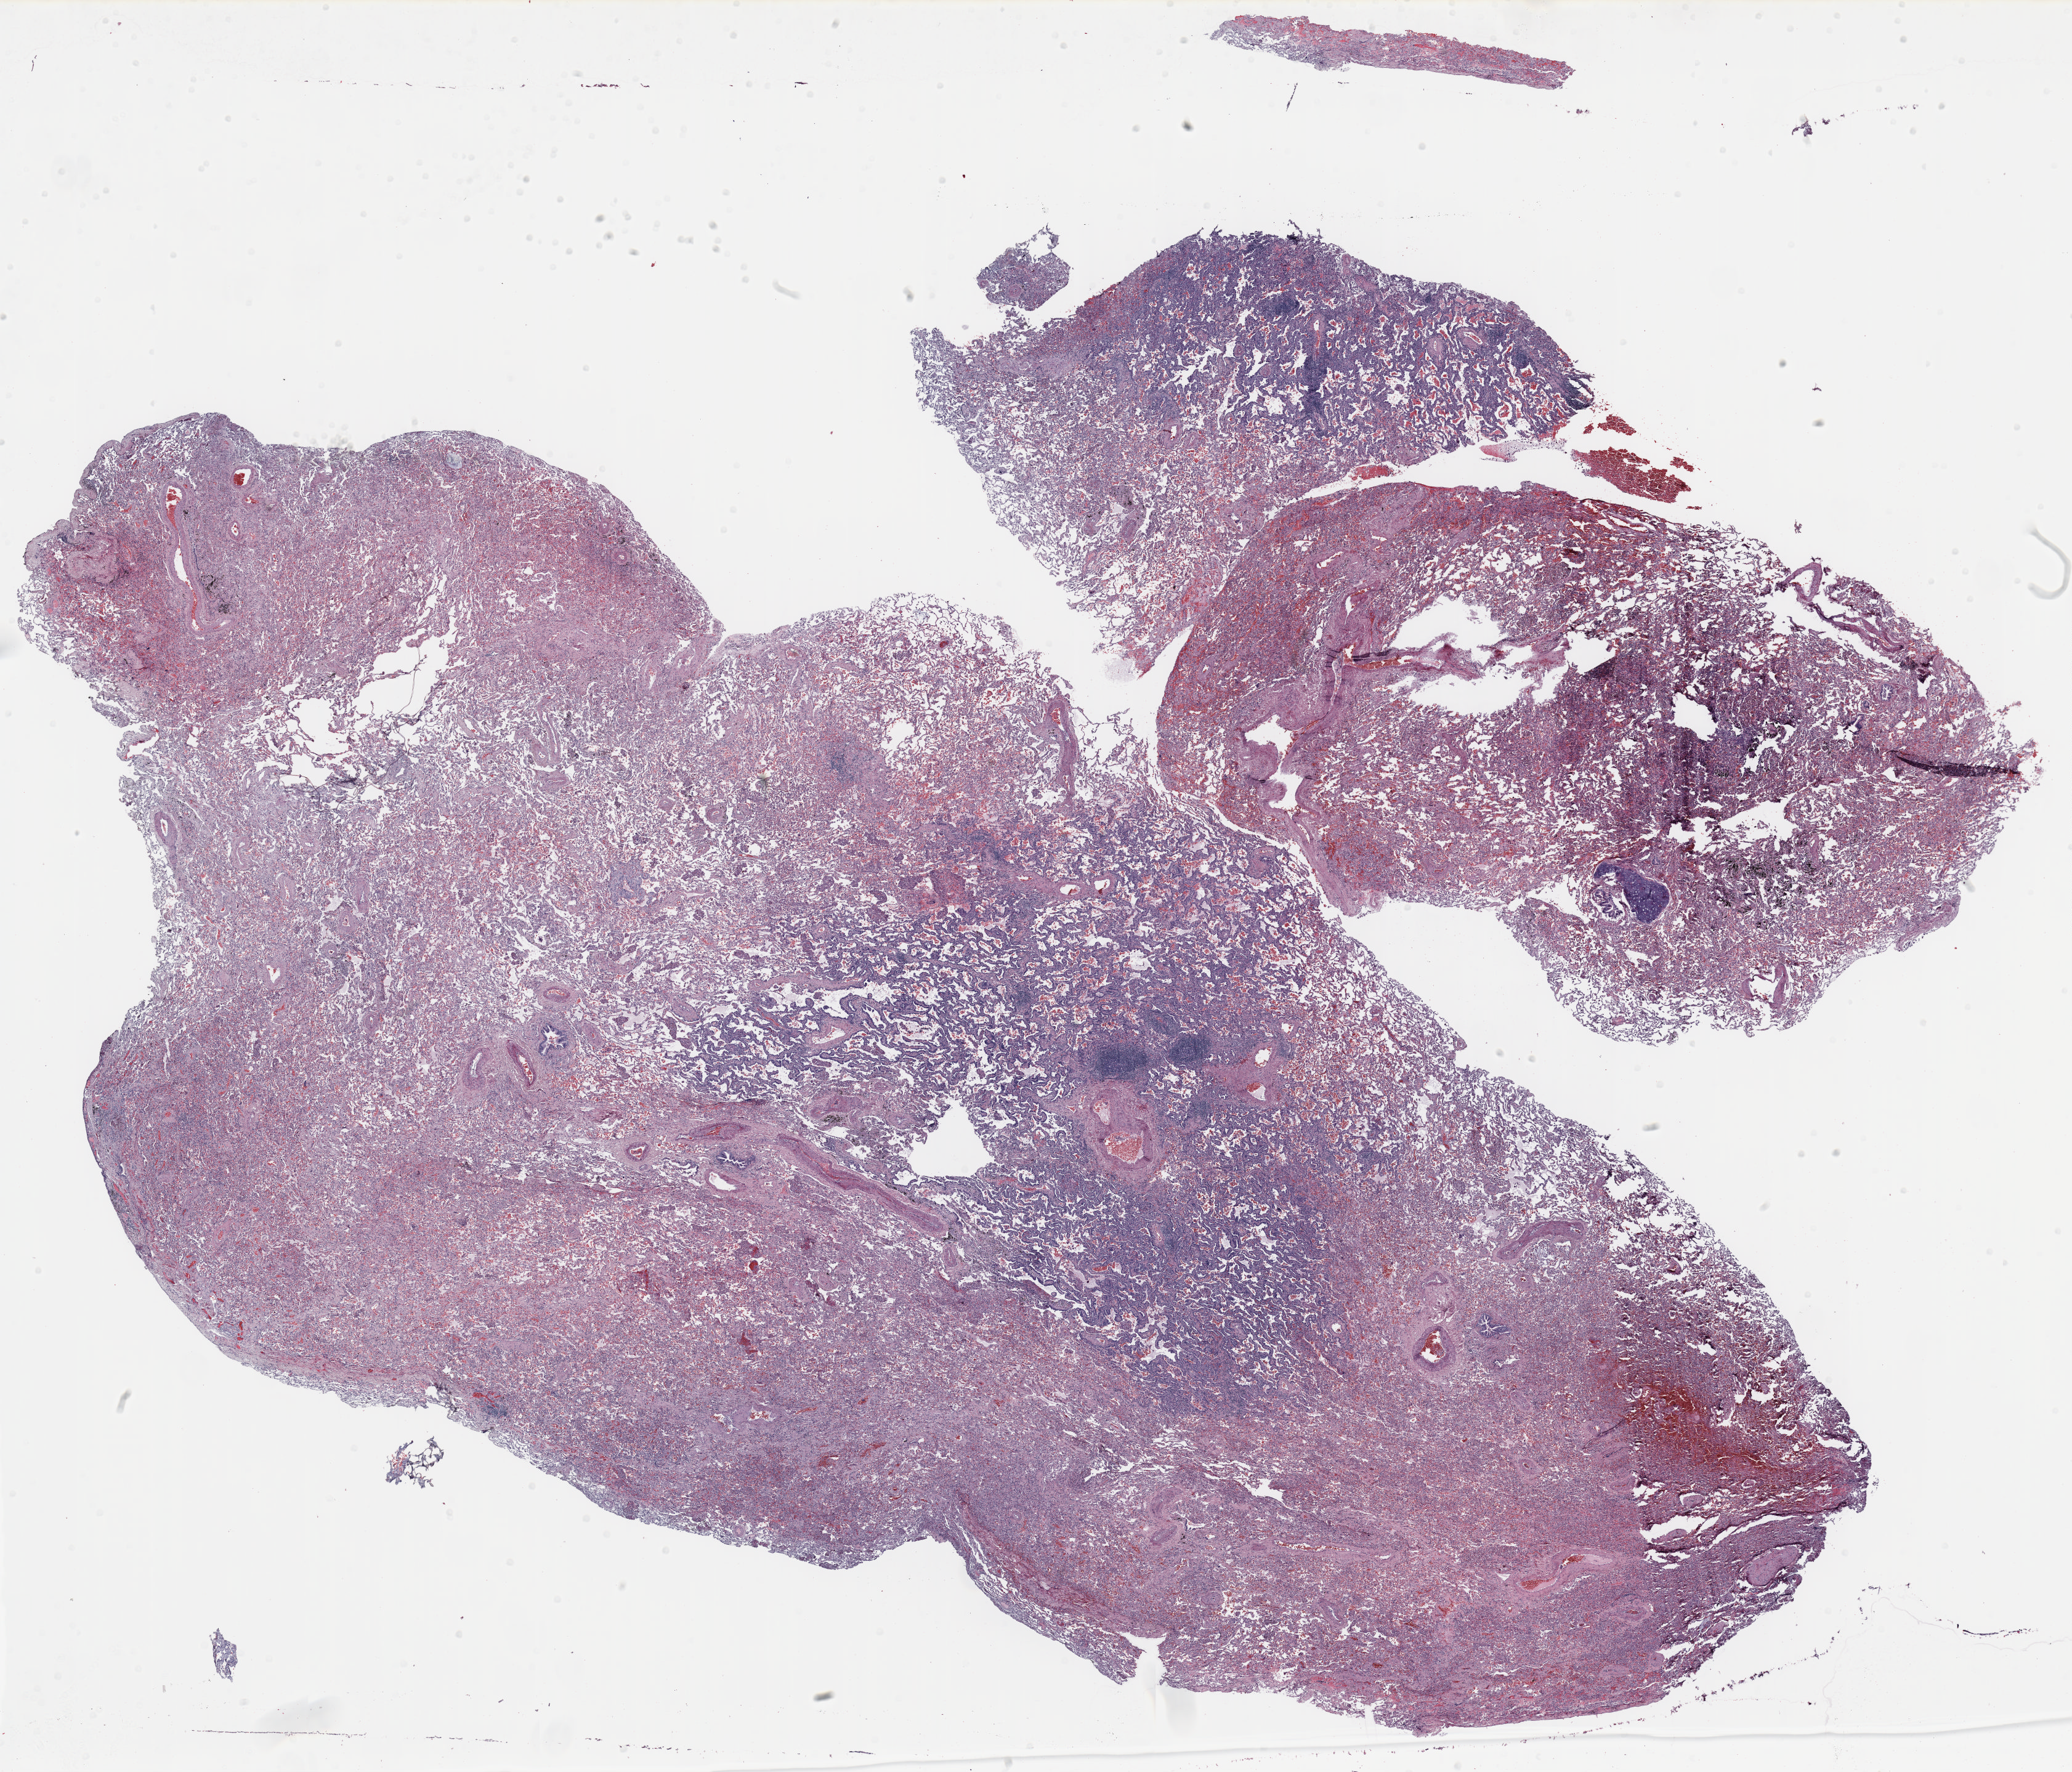
Whole-slide histology image, Hematoxylin and eosin (H&E) stained, whole scanned area (about 27.0 x 23.1 mm, from a 20x scan) shown as a low-resolution overview, formalin-fixed paraffin-embedded (FFPE) section, lung tissue. Male, age 59 at enrolment. Current smoker at enrolment.
Primary tumour location (clinical record): right lower lobe. ICD-O-3 topography: upper lobe of lung (C34.1). Stage (AJCC 6th edition): IA. Tumour size (pathology): 15 mm. Participant's lung-cancer diagnosis: Bronchiolo-alveolar adenocarcinoma, NOS.